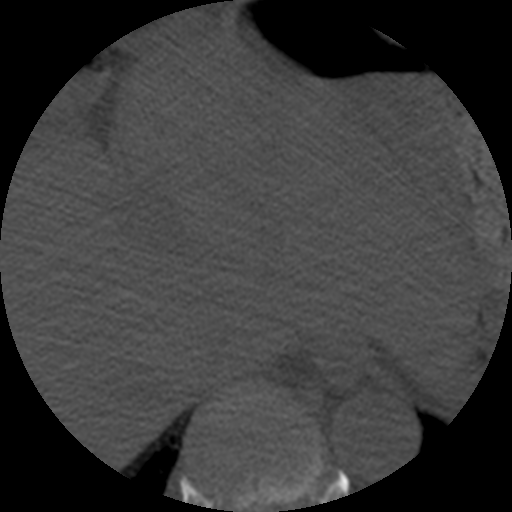
CT including the spine, one axial slice. Slice 278 of 508 in the series (ordered by position). Reconstruction kernel STANDARD. 120 kVp. Bone window (W 1800 / L 400 HU). 1.25 mm slice thickness. 512 × 512 image matrix, field of view 160 × 160 mm. Patient age 57 years. From the clinical record (not read from this slice): primary cancer: prostate.
Outlined on this slice (semi-automatically segmented with operator editing):
- T10 vertebra: box from (x=219, y=406) to (x=223, y=409) px
- T9 vertebra: (x=203, y=442)–(x=323, y=512)